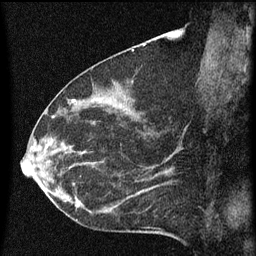
Breast MRI (dynamic contrast-enhanced), one sagittal slice; position 28 of 60 along the scan axis; dynamic contrast-enhanced series, image 2 of 3 at this slice position (ordered by acquisition); 1.5 T; TE 4.2 ms, TR 8 ms; 2 mm slice thickness; 256 × 256 image matrix, field of view 180 × 180 mm. Patient: female, 55 years.
Outlined on this slice (semi-automatic segmentation, software-assisted and operator-edited):
- analysis volume of interest (the breast-tissue region the enhancement analysis was run in; not a lesion): bounding box [x1, y1, x2, y2] px = [51, 156, 145, 217]
- tumour enhancement mask (voxels above the 70 % enhancement threshold inside the analysis volume of interest): [51, 162, 145, 207]